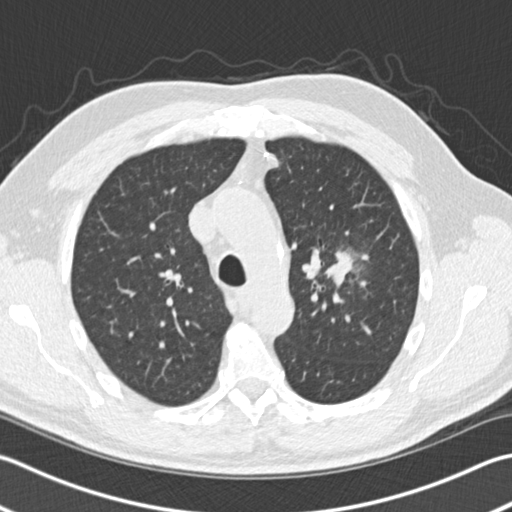
Low-dose screening chest CT, one axial slice. Position 110 of 153 along the scan axis. Reconstruction kernel B30f. 120 kVp. Lung window (W 1500 / L -600 HU). 2 mm slice thickness. 512 × 512 image matrix, field of view 346 × 346 mm.
Outlined on this slice (expert manual segmentation):
- lesion 1 (tumor, upper lobe of left lung): bounding box (x1, y1, x2, y2) in pixels: (326, 252, 353, 284)